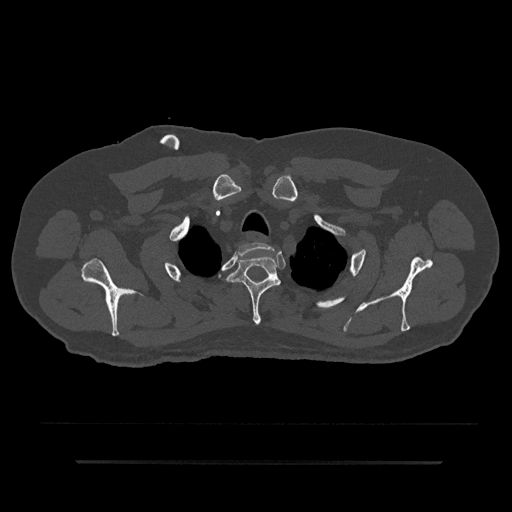
CT including the spine, one axial slice. Slice 700 of 797 in the series (ordered by position). Reconstruction kernel Br40s/3. 120 kVp. Bone window (W 1800 / L 400 HU). 0.5 mm slice thickness. 512 × 512 image matrix, field of view 464 × 464 mm. Patient: male, 59 years. Case-level facts recorded for this patient, not image findings: primary cancer: bile ducts; vertebrae with lytic lesions (as recorded): T10.
Annotated regions visible in this slice (semi-automatic segmentation, software-assisted and operator-edited):
- T1 vertebra: bounding box (x1, y1, x2, y2) in pixels: (238, 242, 274, 257)
- T2 vertebra: (226, 254, 281, 325)